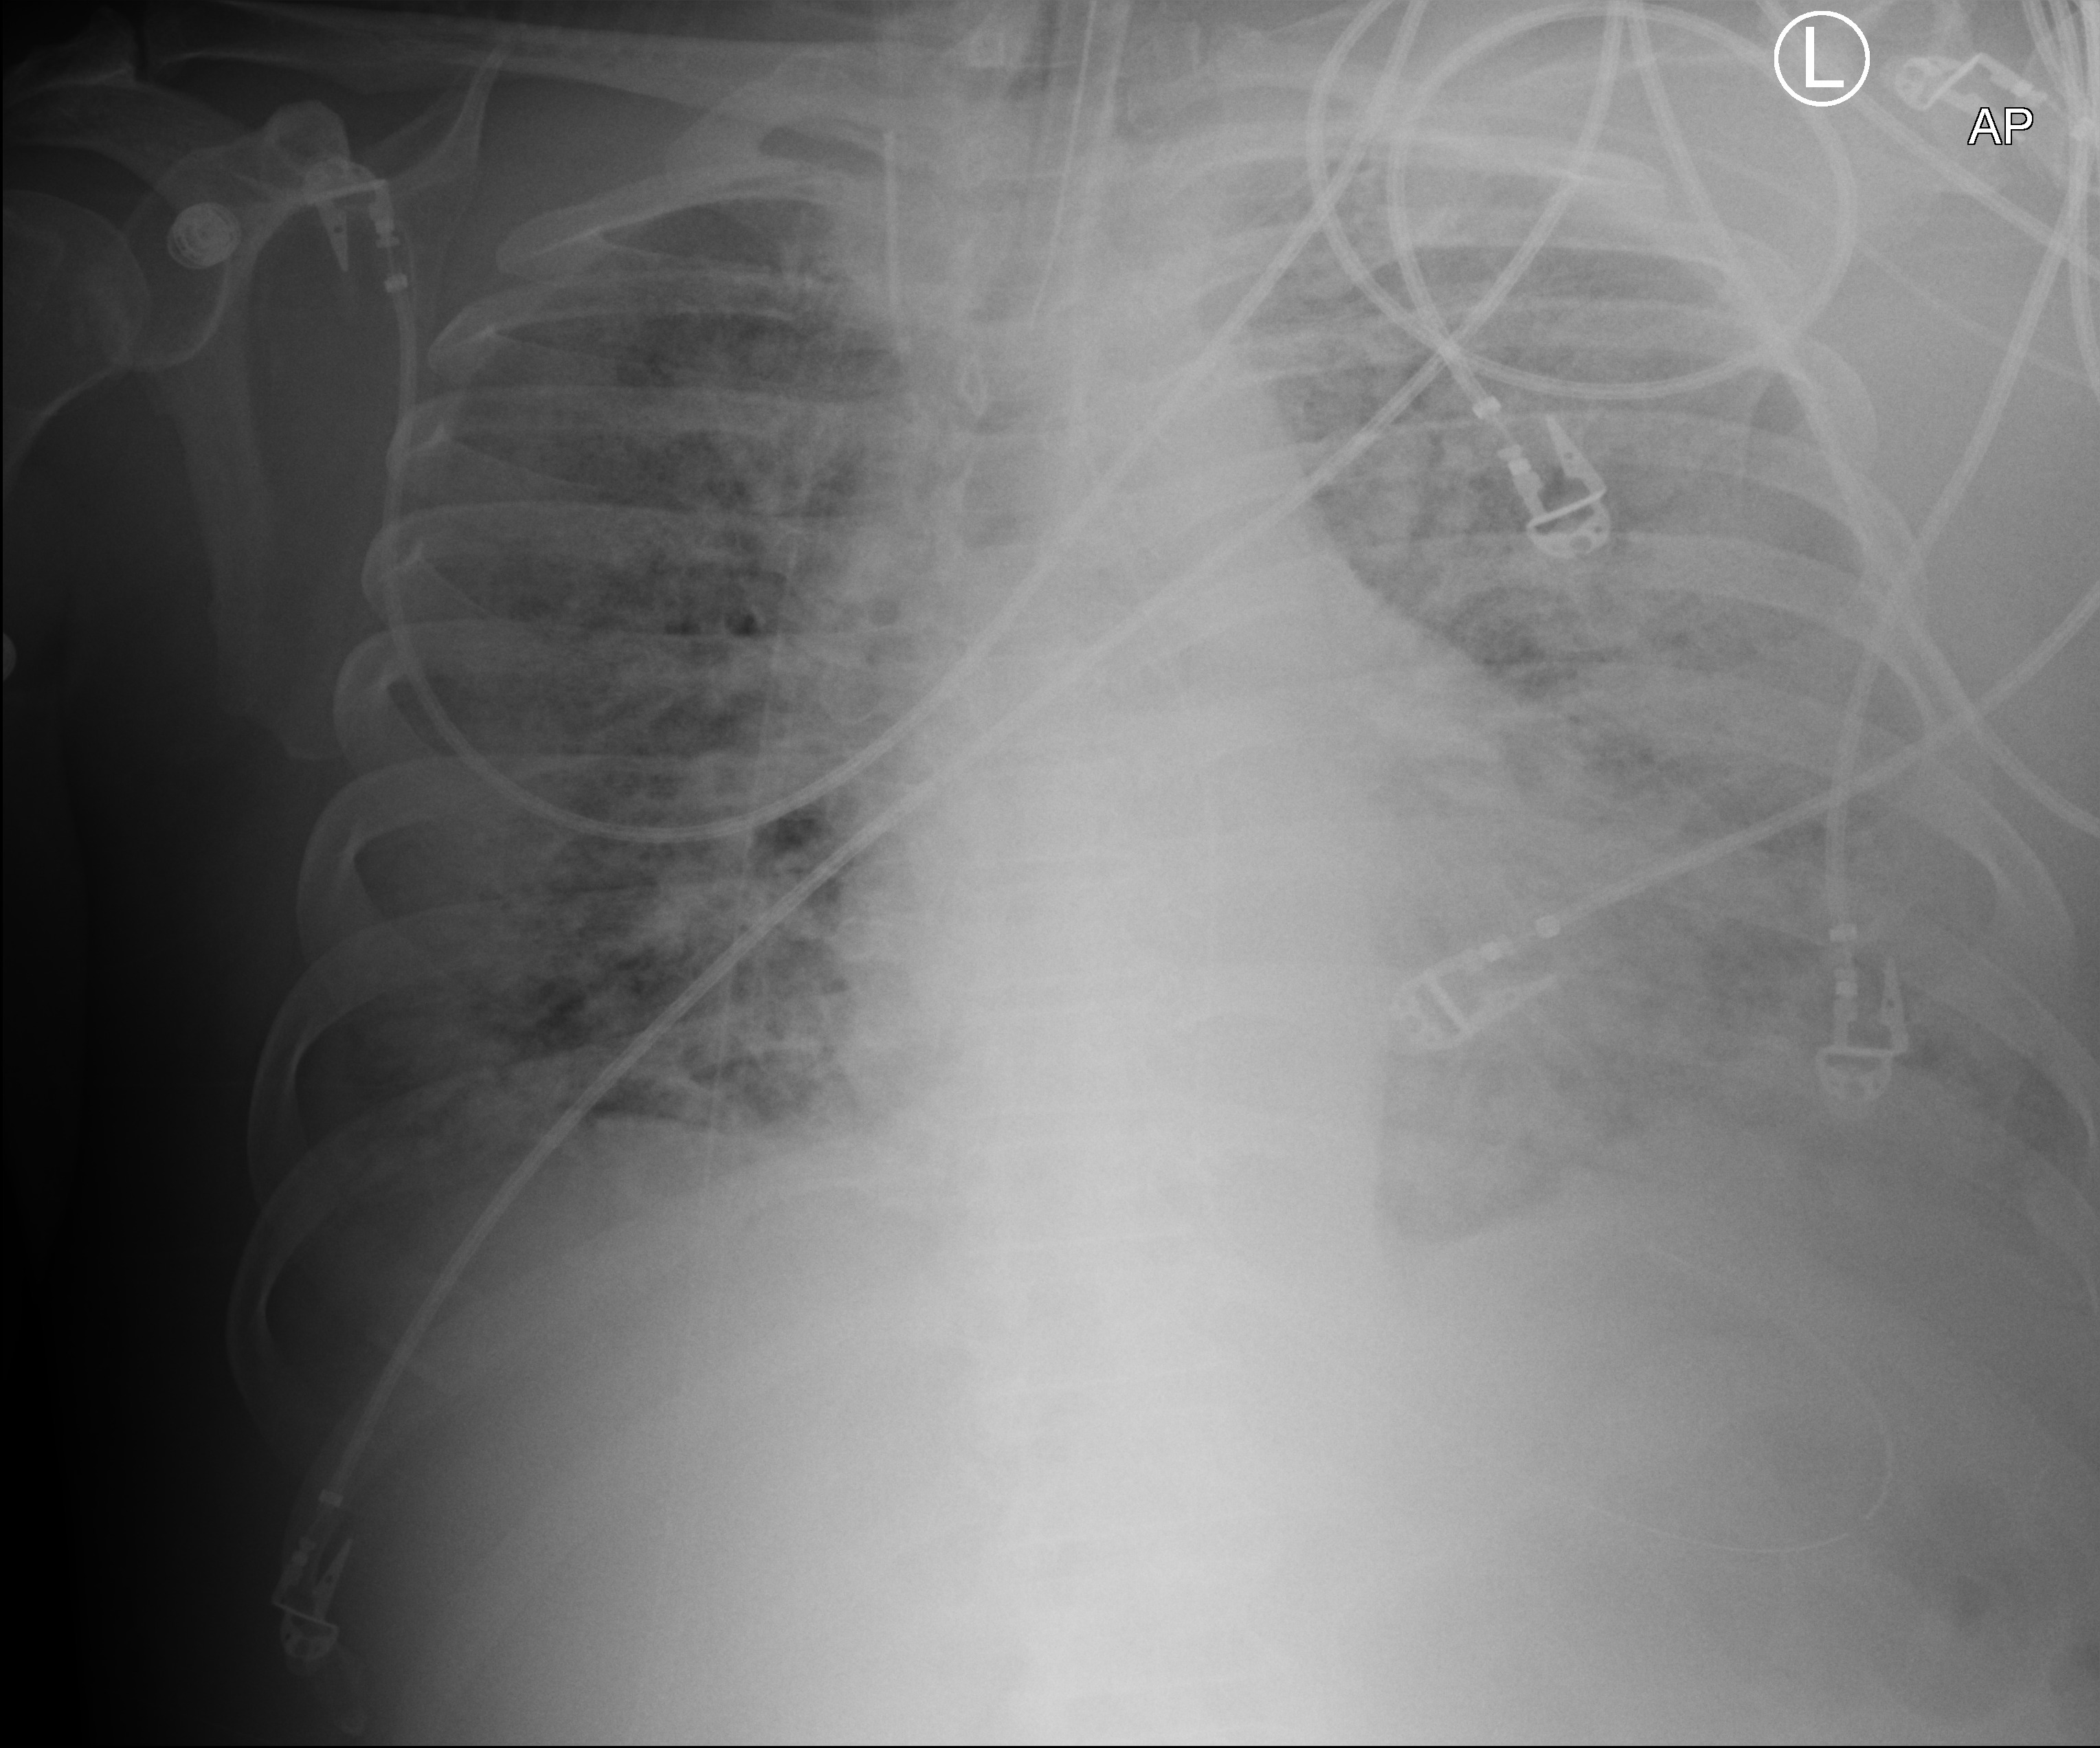
Bedside chest radiograph (computed radiography); anteroposterior (AP) projection. Male patient hospitalised with COVID-19, age 60–74 years.
Hospital-stay facts (about this admission, not read from this image; timing relative to this image not recorded):
- COPD (admission record): no